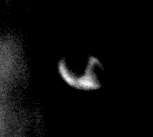
Crop from a digitized film mammogram around one marked abnormality; left breast; MLO view; BI-RADS breast density category 1 (scale 1–4).
Calcifications, morphology lucent center; BI-RADS assessment category 2; benign; no additional work-up was recommended (benign without callback).